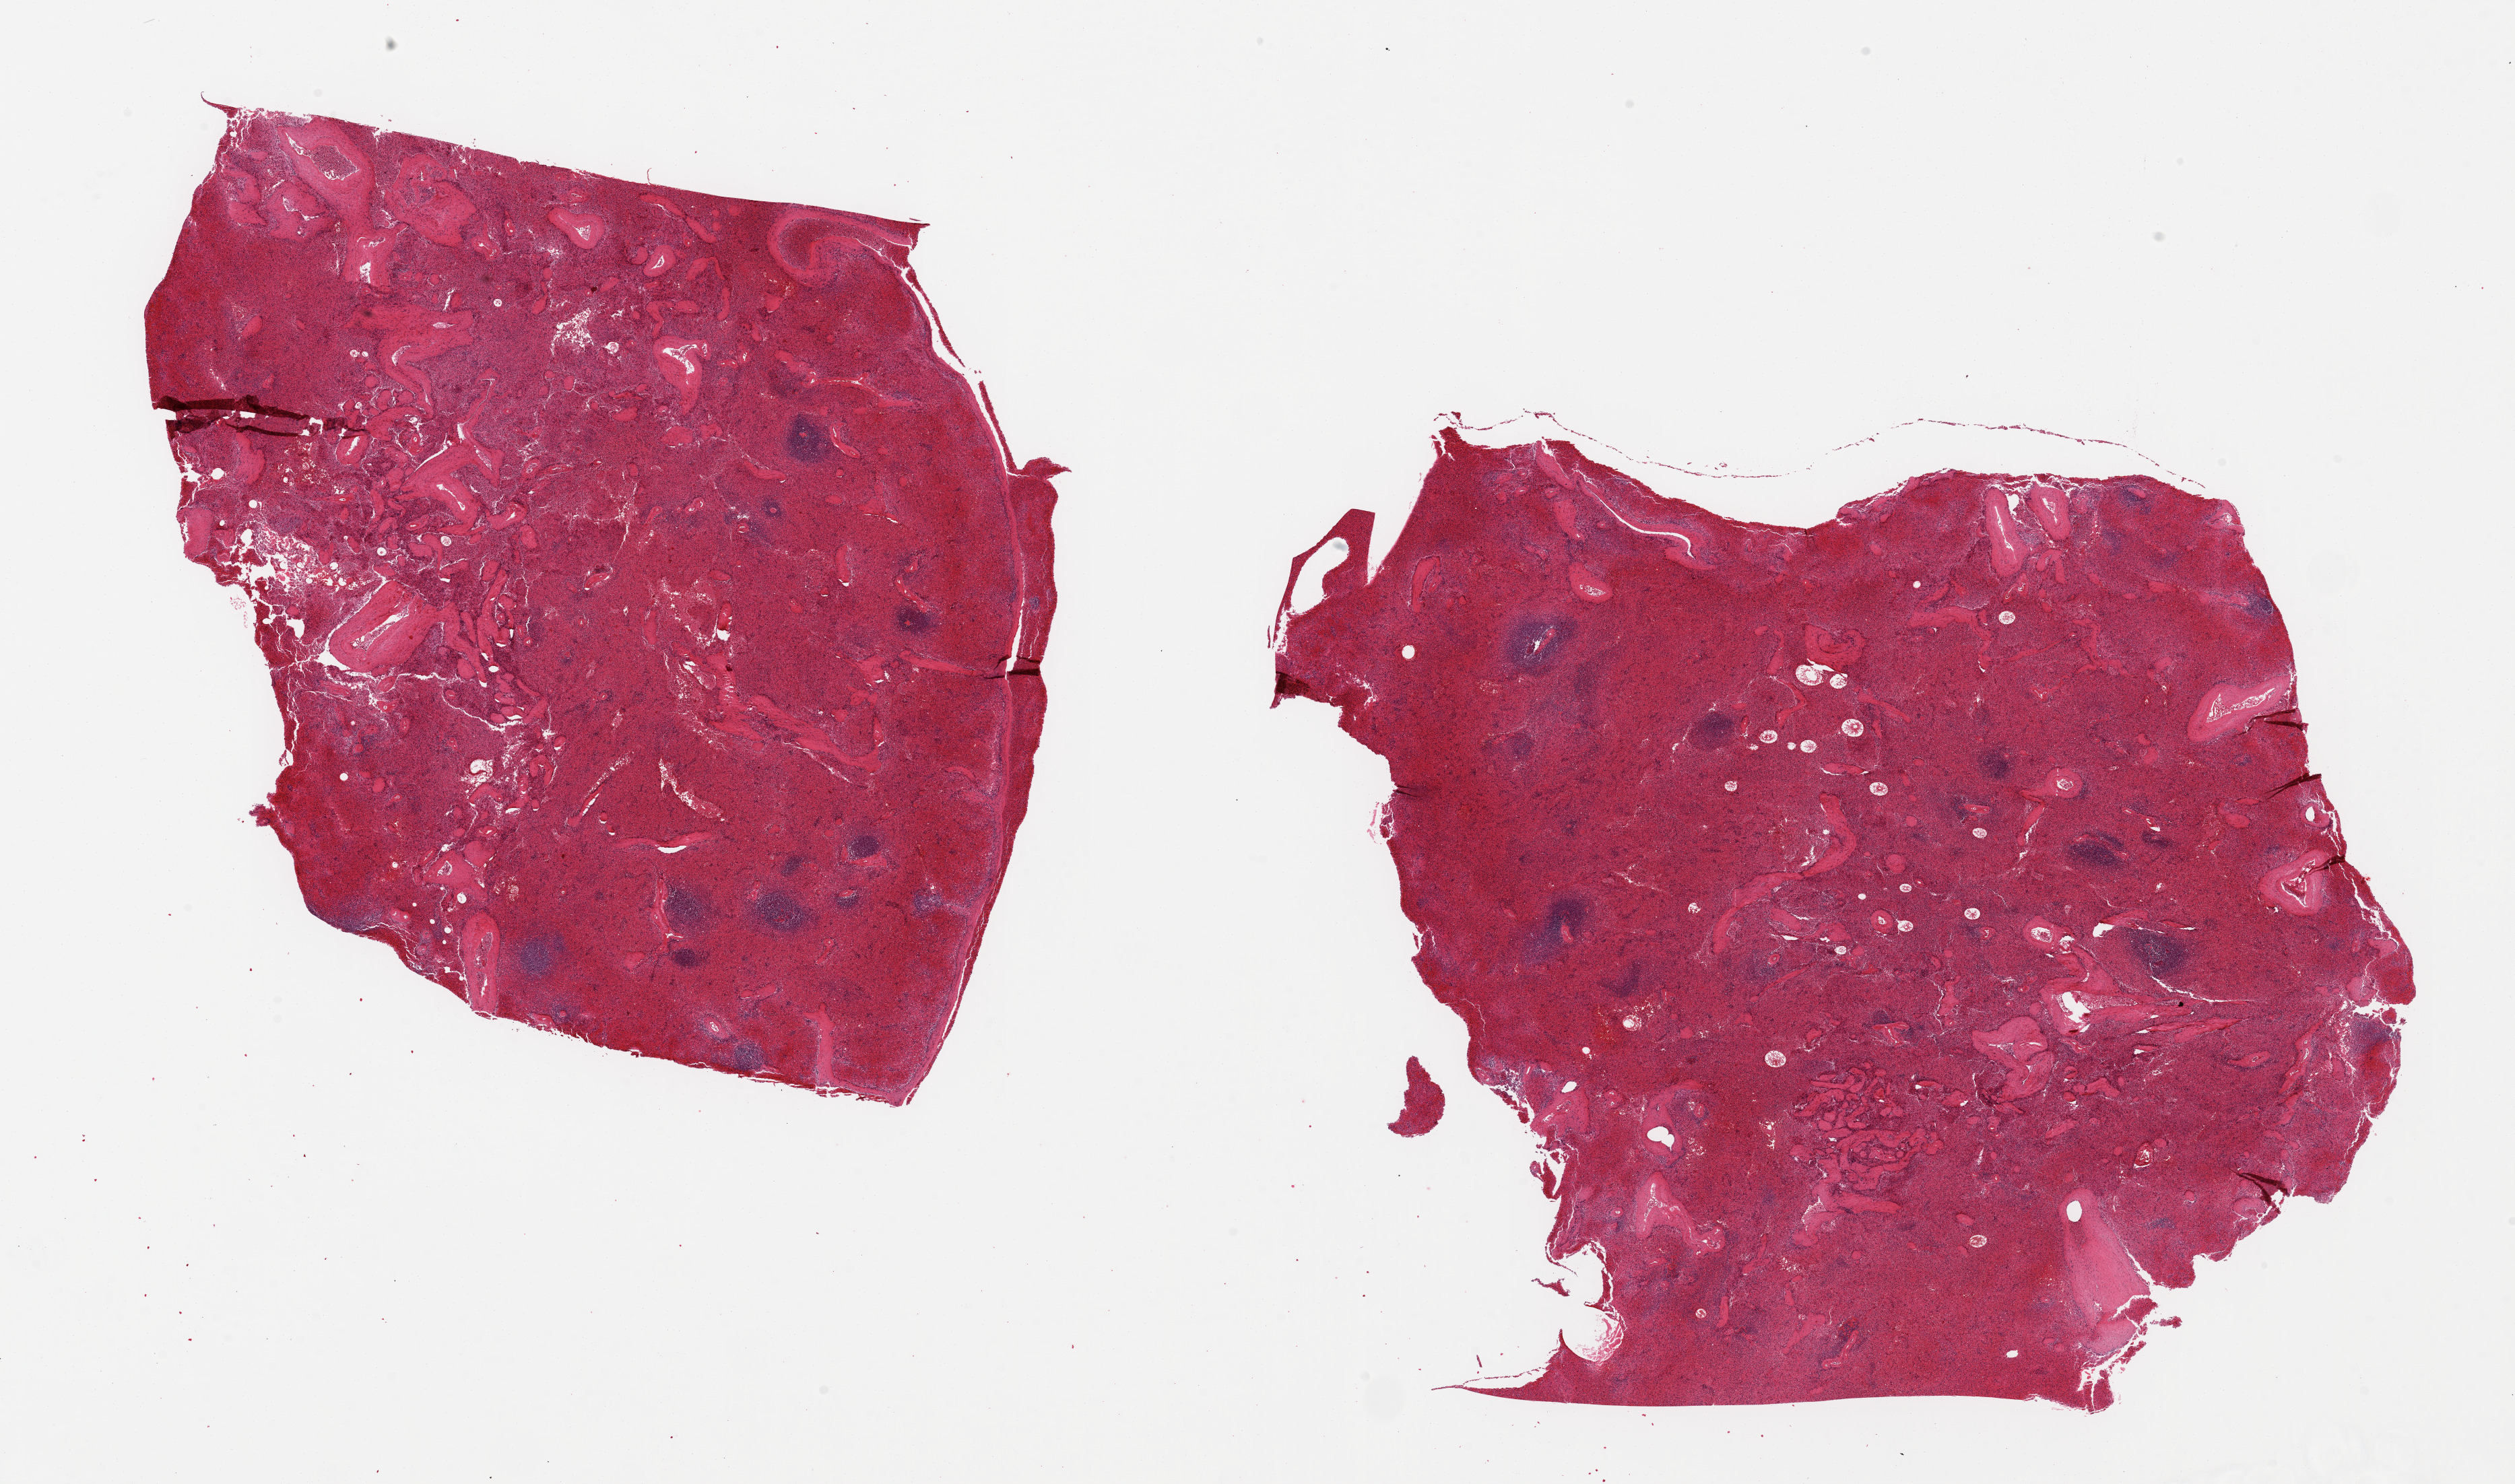
Digitized hematoxylin and eosin (H&E)-stained section, brightfield, a low-resolution overview of the entire scanned area, about 29.5 x 17.4 mm (from a 20x scan), PAXgene-fixed, paraffin-embedded tissue, section of spleen (target tissue), donor tissue sample. Female donor.
Pathologist's review note for this sample: 2 ~10x9mm aliquots, marked congestion of red pulp.